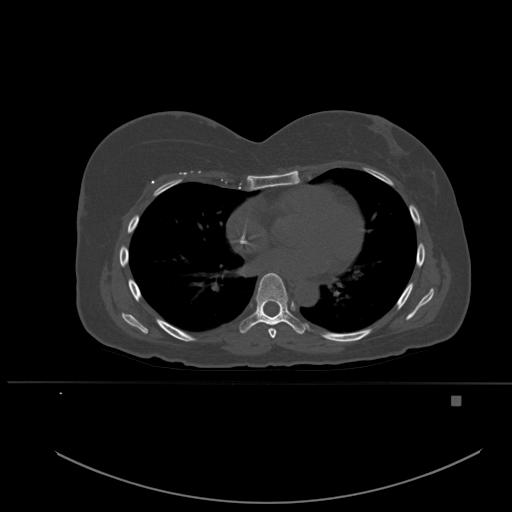
CT including the spine, one axial slice. Slice 338 of 651 in the series (ordered by position). Bone window (W 1800 / L 400 HU). 1.5 mm slice thickness. 512 × 512 image matrix, field of view 443 × 443 mm. Patient: female, 49 years. From the clinical record (not read from this slice): primary cancer: breast; vertebrae with lytic lesions (as recorded): L3, T12, L4.
Structures marked on this image (semi-automatically segmented with operator editing):
- T6 vertebra: bounding box [x1, y1, x2, y2] px = [268, 328, 277, 338]
- T7 vertebra: [239, 273, 306, 334]